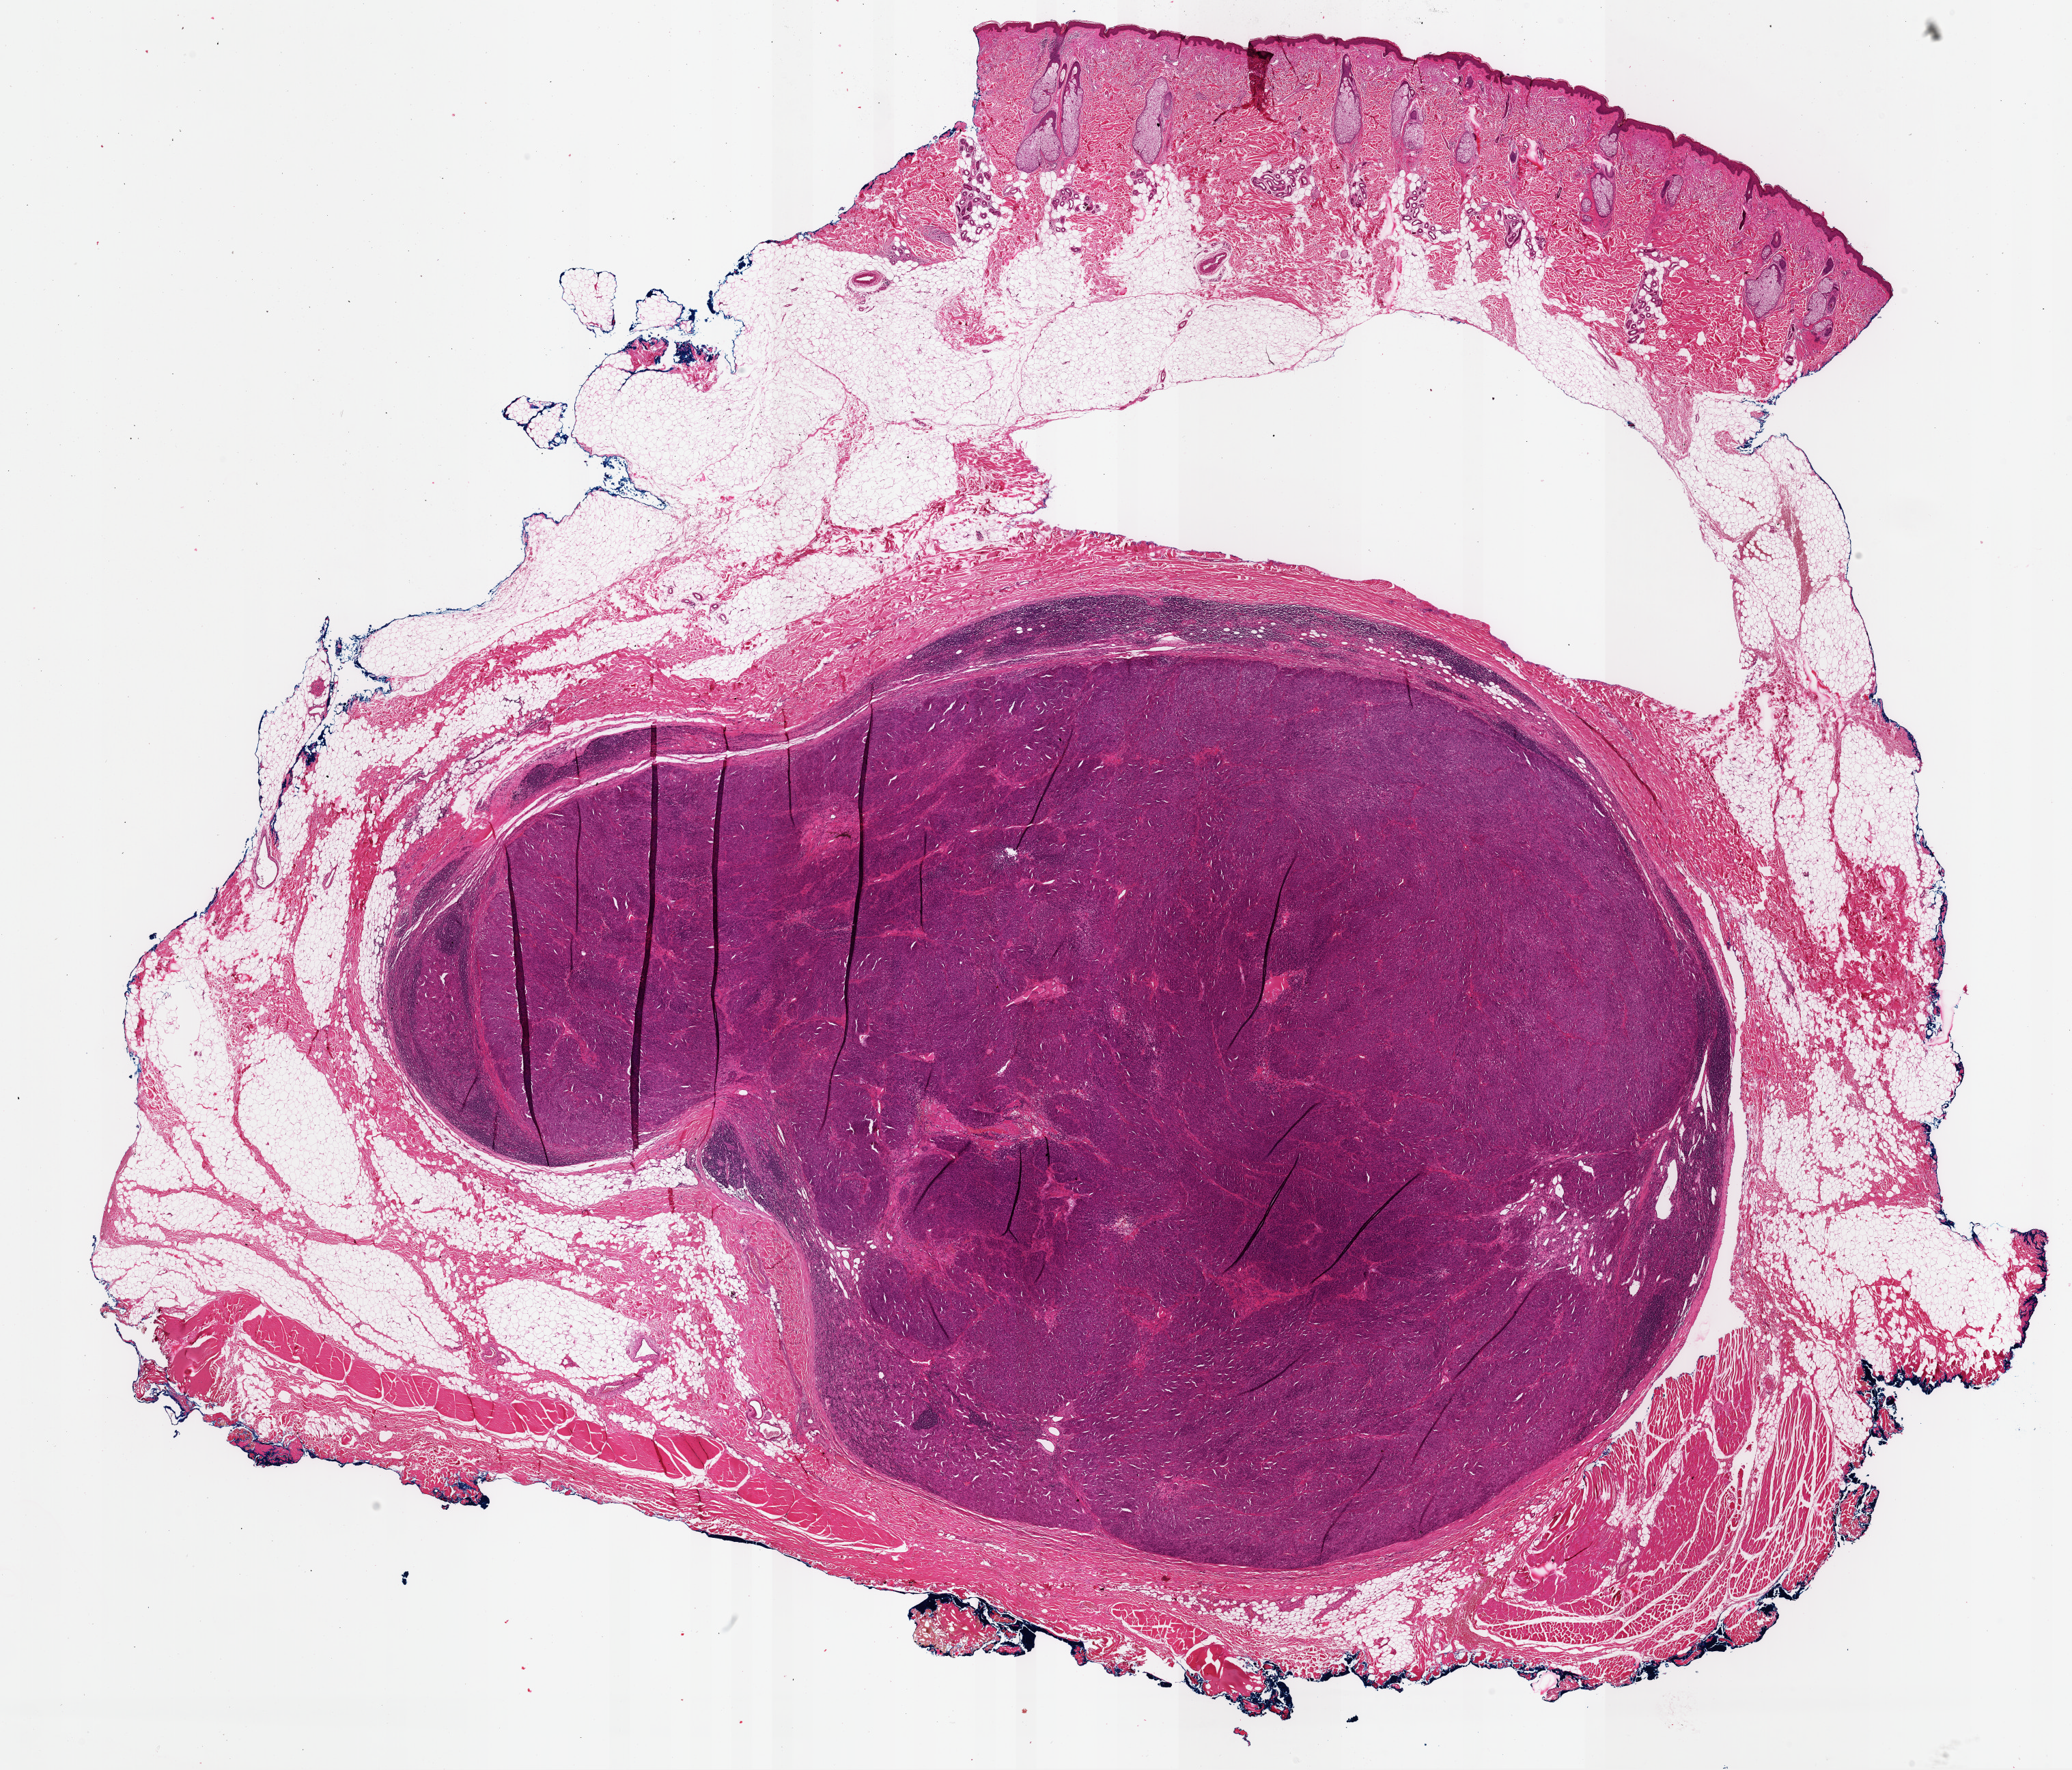
Digitized H&E-stained tissue section (whole slide), whole scanned area (about 24.0 x 20.5 mm) shown as a low-resolution overview, formalin-fixed paraffin-embedded (FFPE) diagnostic section, sample: primary tumour, skin. Patient: male, age at initial diagnosis 50 years.
TNM: T0 N1b M0. Diagnosis: Malignant melanoma, NOS. AJCC pathologic stage: III.